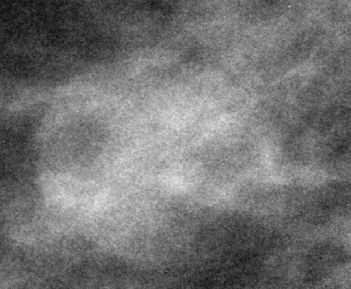
Cropped region of a digitized screen-film mammogram centred on a radiologist-marked abnormality; right breast; MLO view.
- Marked abnormality: mass, shape oval, margins circumscribed; BI-RADS assessment category 3; pathology result (as recorded, not read from the image): benign.